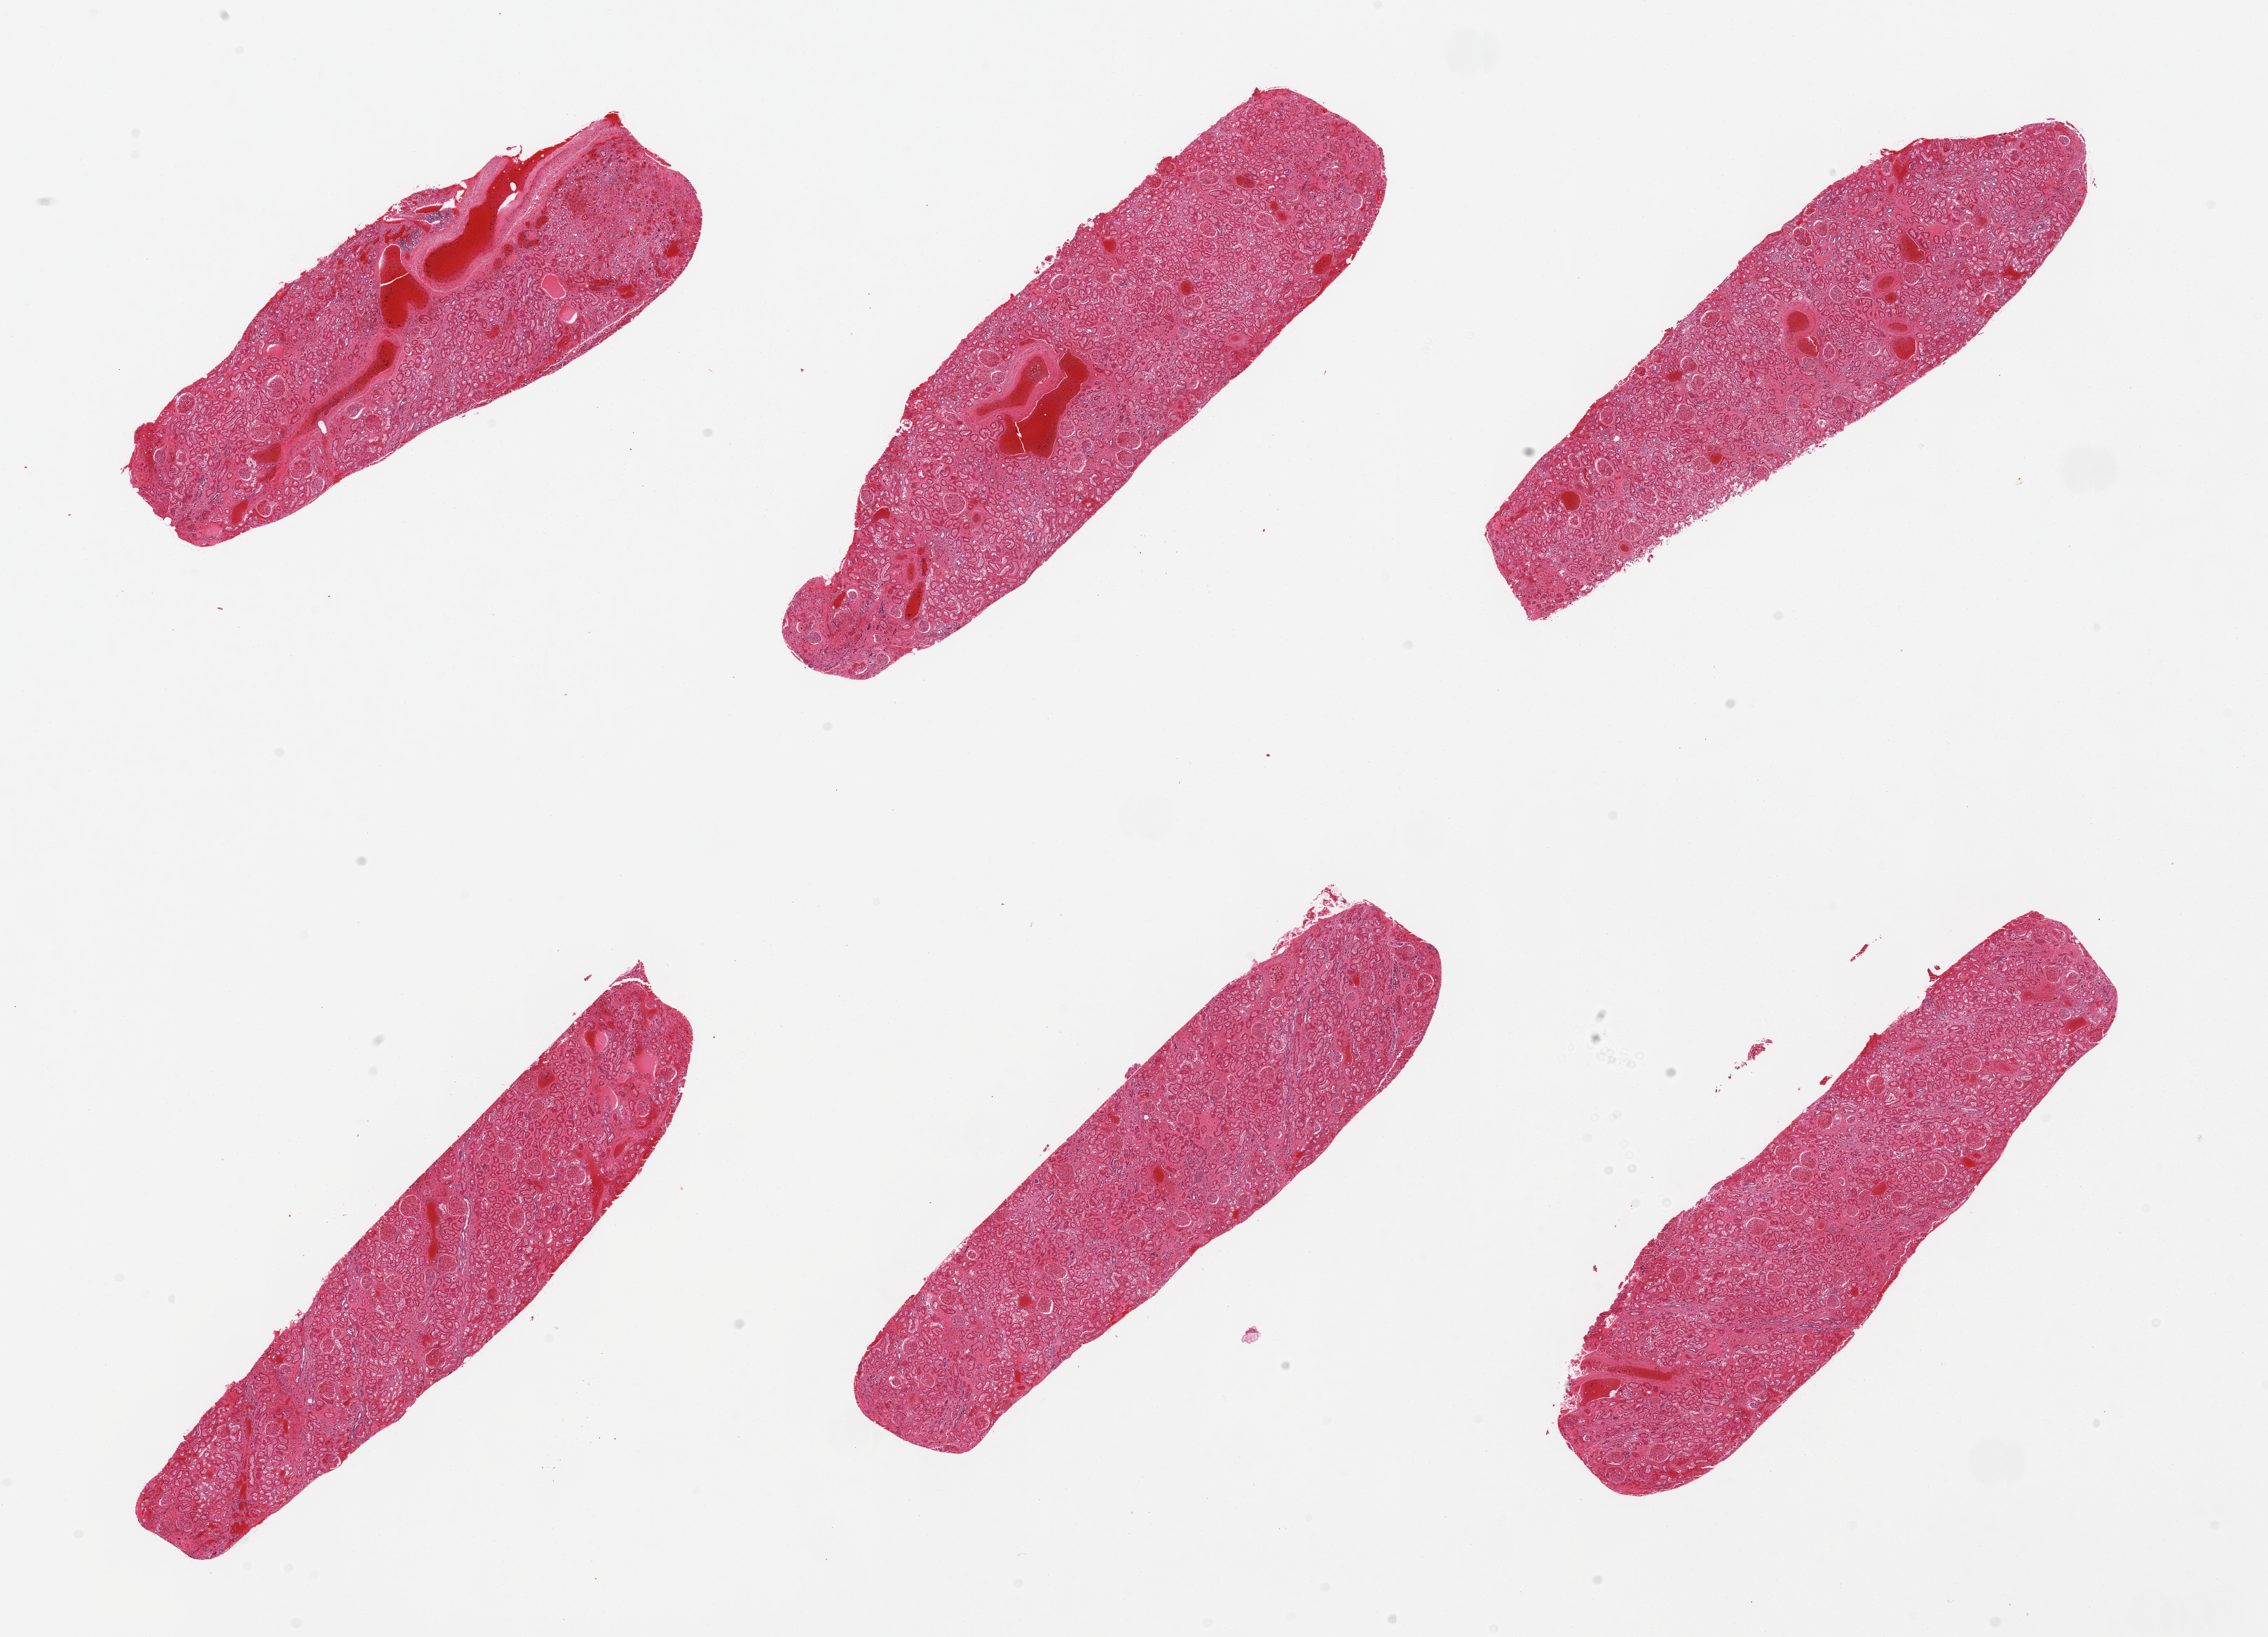
Digitized H&E-stained section, a low-resolution overview of the entire scanned area, about 25.6 x 18.5 mm (from a 20x scan); PAXgene-fixed, paraffin-embedded tissue; section of renal cortex (target tissue); donor tissue sample. Male donor.
Review note (as recorded): 6 pieces, glomeruli present.